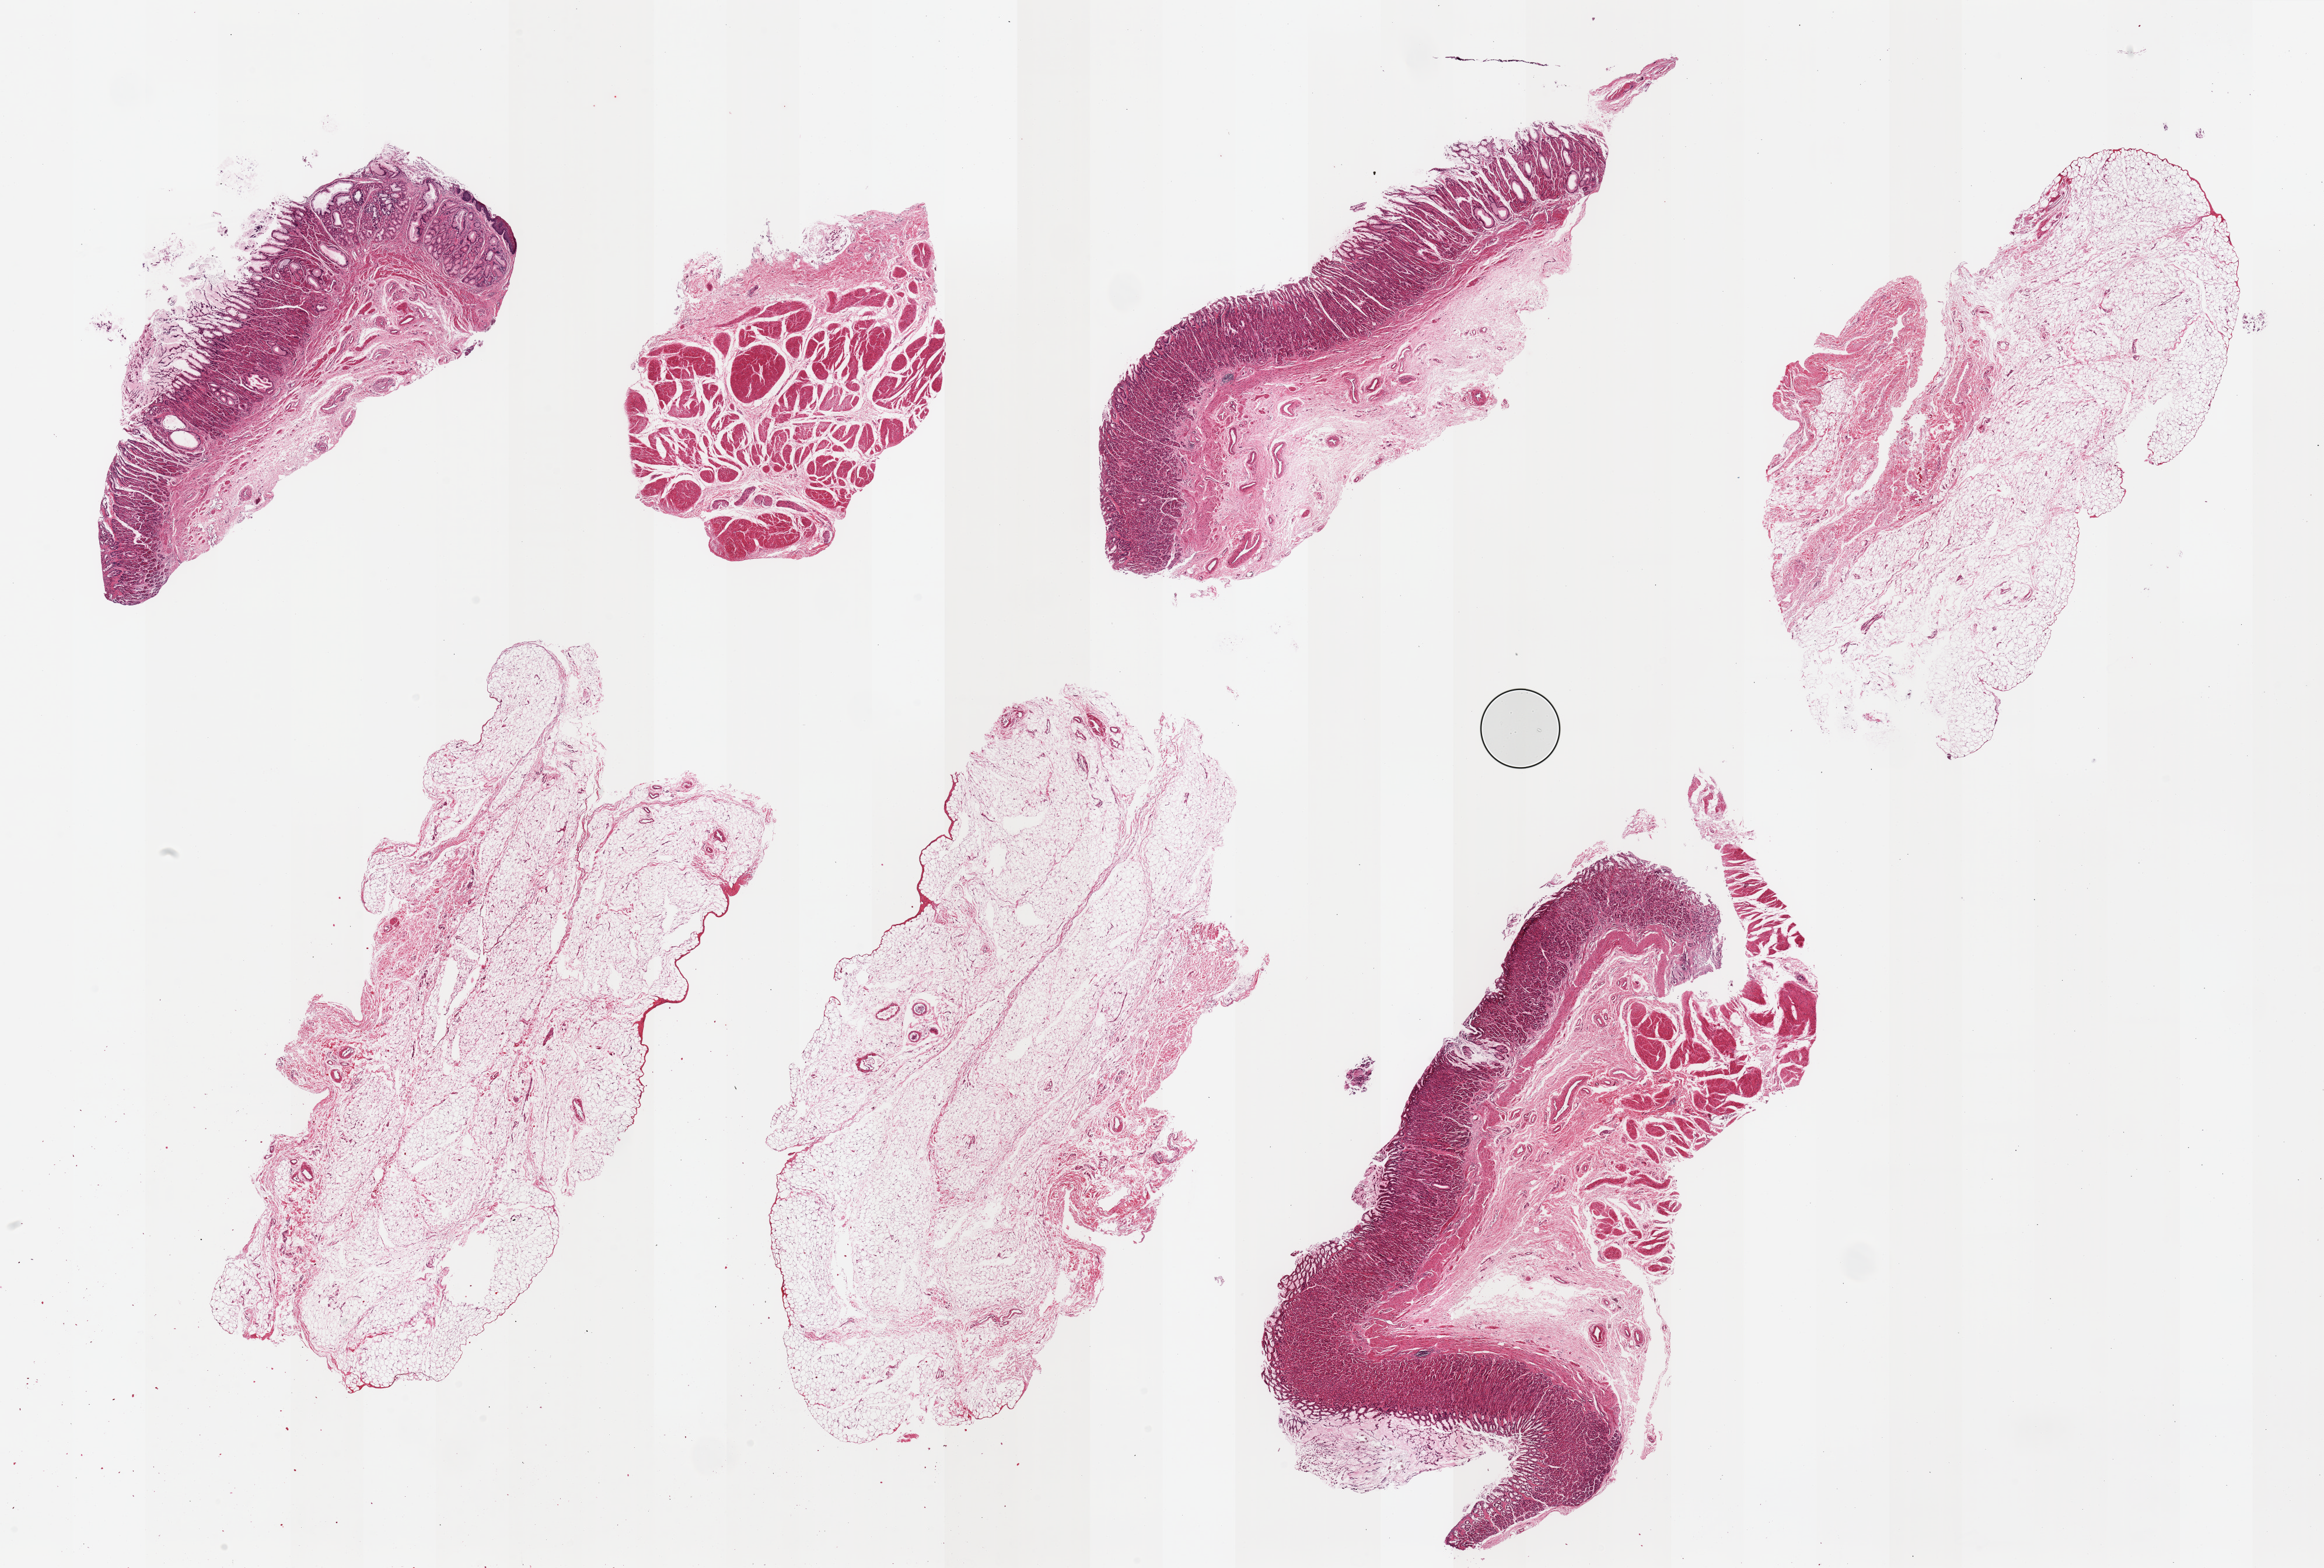
Digitized H&E-stained section — low-resolution overview of the scanned area, about 31.5 x 21.3 mm. PAXgene-fixed, paraffin-embedded tissue. Sampled site (target tissue): gastroesophageal junction. Tissue donor sample. Female donor.
Pathologist's review note for this sample: 6 pieces, no target muscularis, fragements of gastric mucosa, predominantly adipose tissue.